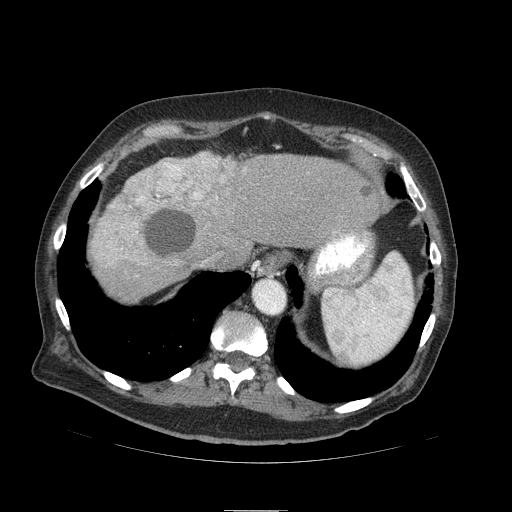
Contrast-enhanced abdominal CT (liver protocol), one axial slice. Position 75 of 103 along the scan axis. Reconstruction kernel STANDARD. Soft-tissue window (W 400 / L 40 HU). 512 × 512 image matrix, field of view 440 × 440 mm. From the clinical record (not read from this slice): diagnosis: hepatocellular carcinoma (patient treated with transarterial chemoembolisation; whether this scan precedes or follows treatment is not stated here); TNM stage (as recorded): Stage-IIIA; Child-Pugh class: B; tumour differentiation: well differentiated; tumour nodularity: multinodular.
Structures marked on this image (semi-automatic segmentation, software-assisted and operator-edited):
- liver parenchyma outside the tumour (the mass and vessels are separate outlines, so this box may not span the whole liver): bounding box <90,150,388,300> (left, top, right, bottom; pixels)
- mass: <93,153,251,263>